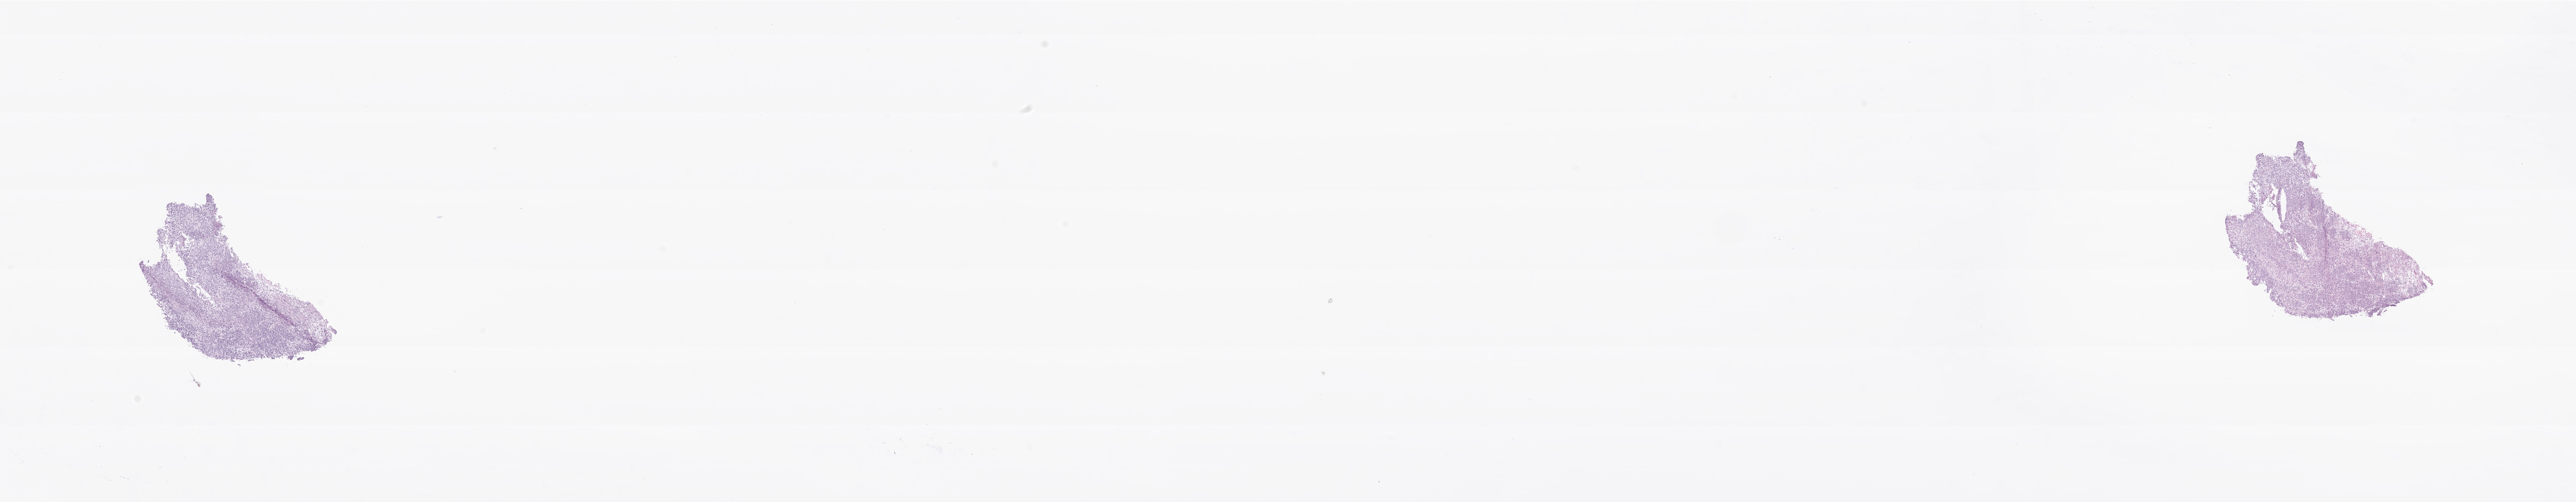
Haematoxylin and eosin whole-slide image of tumor tissue from the brain, whole scanned area (about 35.1 x 6.8 mm) shown as a low-resolution overview. Frozen section (OCT-embedded). Patient female; age 148 months (12 years 4 months).
- diagnosis (ICD-O-3 morphology term): Glioblastoma, NOS